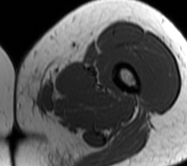
MRI of an extremity soft-tissue mass, one axial slice. Slice 6 of 62 in the series (ordered by position). MR volume resampled by the dataset authors to the PET/CT grid (not the native acquisition matrix). 3.27 mm slice thickness. 187 × 166 image matrix, field of view 183 × 162 mm. Female patient. Case-level facts recorded for this patient, not image findings: histological type: leiomyosarcoma; grade: high; site of the primary tumour: groin.
Outlined on this slice (expert contour drawn on MRI and transferred to this co-registered scan by the dataset authors):
- gross tumour volume including surrounding oedema: box from (x=16, y=87) to (x=44, y=113) px